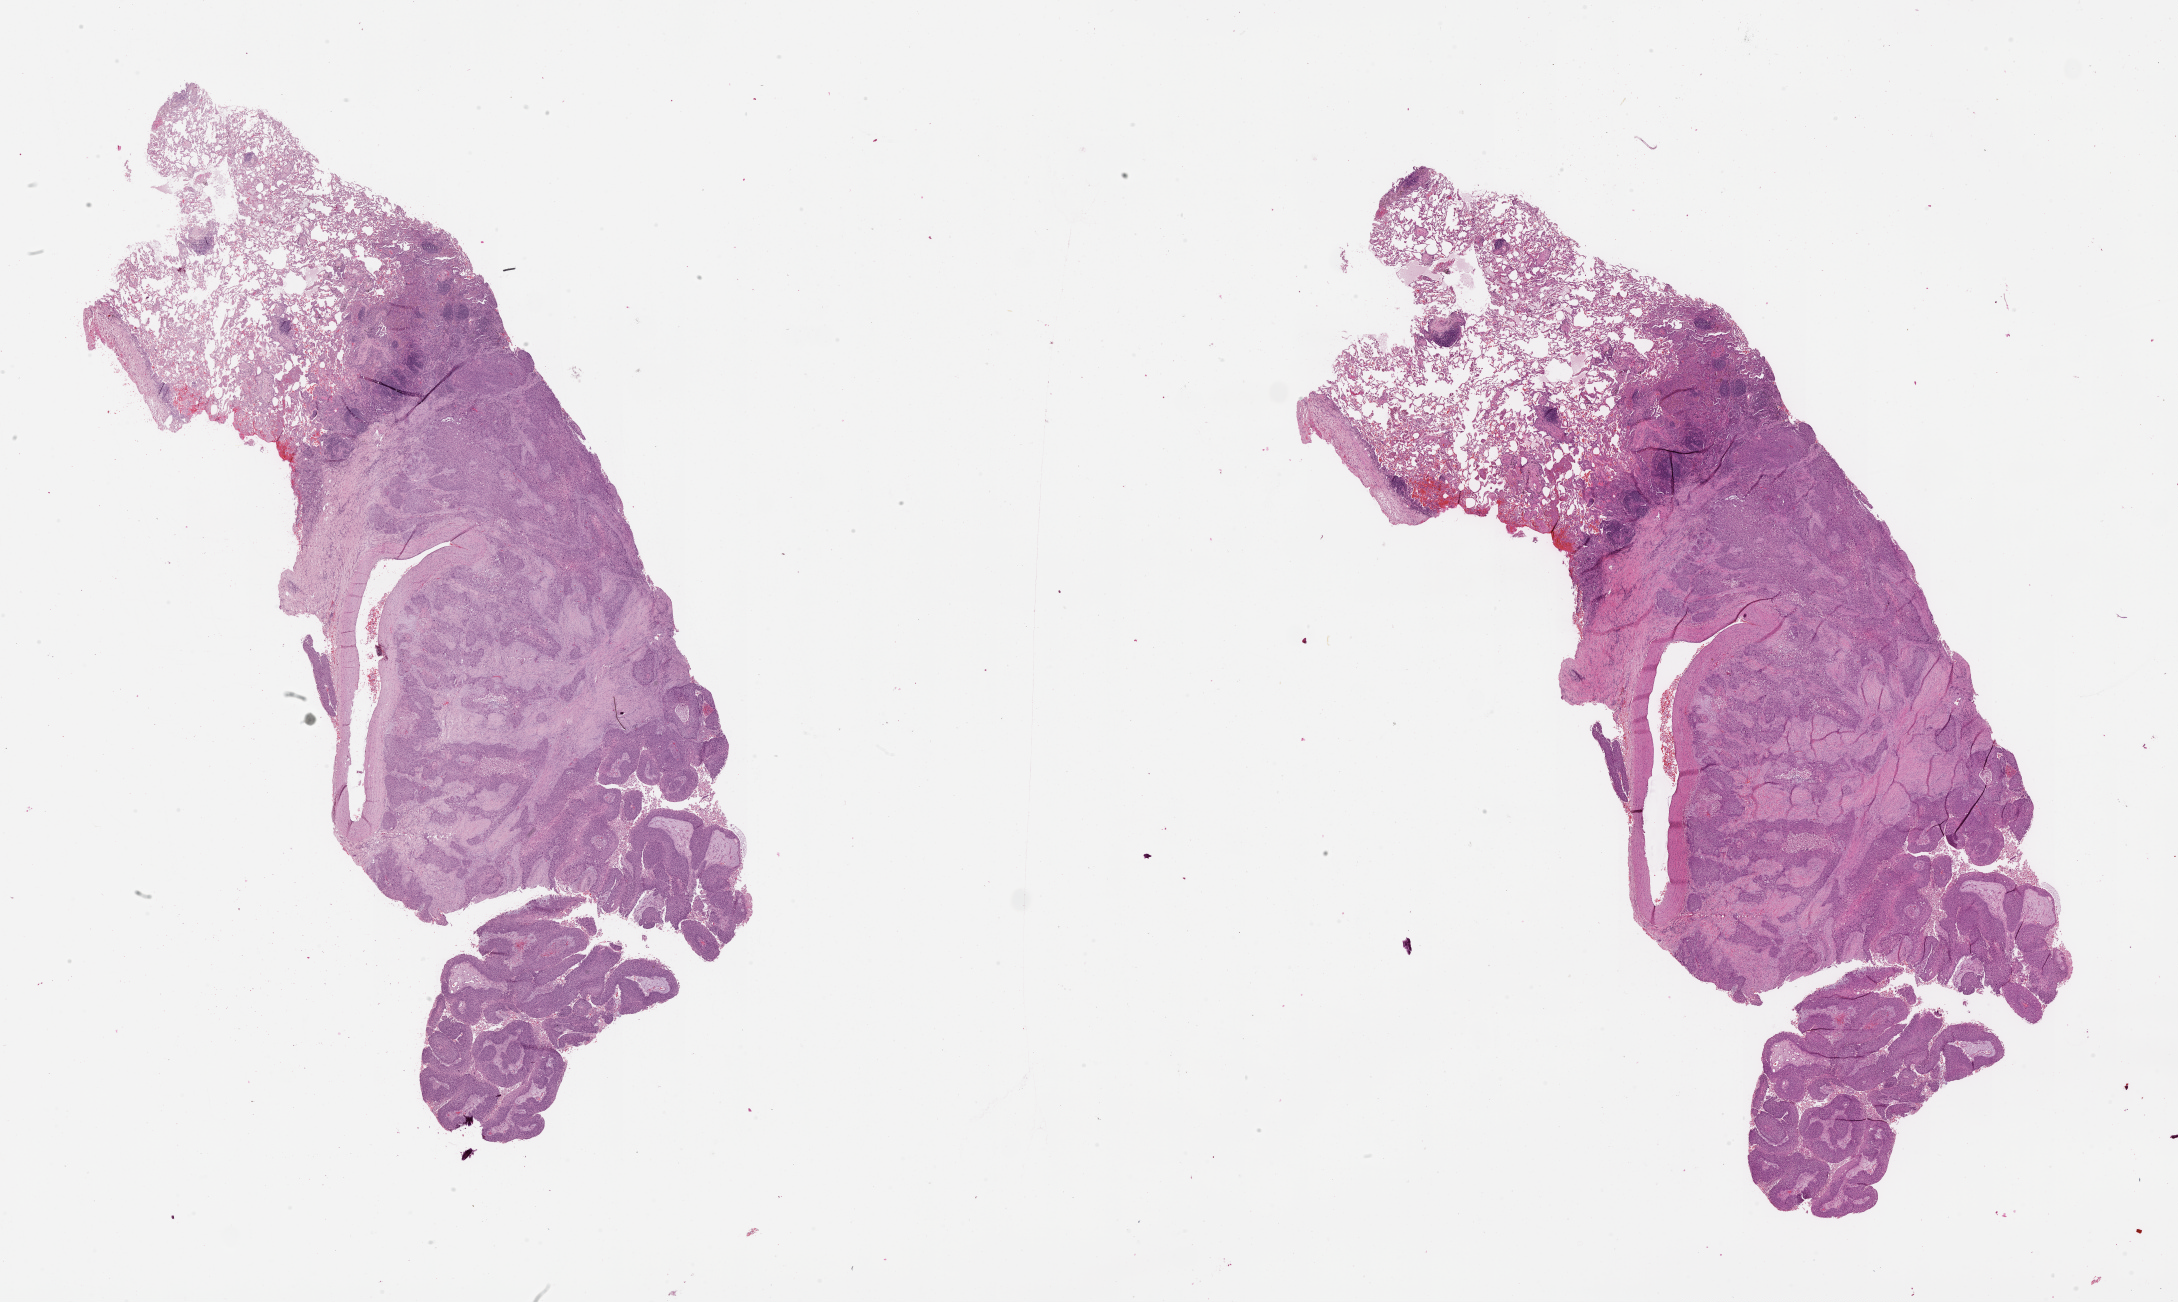
Digitized H&E tissue section (whole slide) — low-resolution overview of the scanned area, about 35.1 x 21.0 mm. Tumour tissue sample, lung. 43-year-old male patient.
* patient diagnosis (cohort enrolment): squamous cell carcinoma (lung)